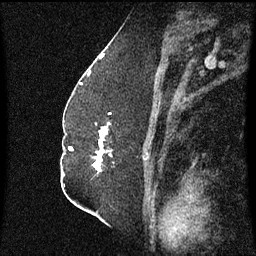
Breast MRI (dynamic contrast-enhanced), one sagittal slice. Position 34 of 60 along the scan axis. Dynamic contrast-enhanced series, image 2 of 3 at this slice position (ordered by acquisition). 1.5 T. TE 4.2 ms, TR 8.4 ms. 2.3 mm slice thickness. 256 × 256 image matrix, field of view 200 × 200 mm. Patient: female, 52 years. From the clinical record (not read from this slice): setting: breast cancer imaged before/during neoadjuvant chemotherapy; receptor status: HR-positive, HER2-negative.
Outlined on this slice (semi-automatically segmented with operator editing):
- analysis volume of interest (the breast-tissue region the enhancement analysis was run in; not a lesion): bounding box <93,114,111,173> (left, top, right, bottom; pixels)
- tumour enhancement mask (voxels above the 70 % enhancement threshold inside the analysis volume of interest): <93,124,109,171>